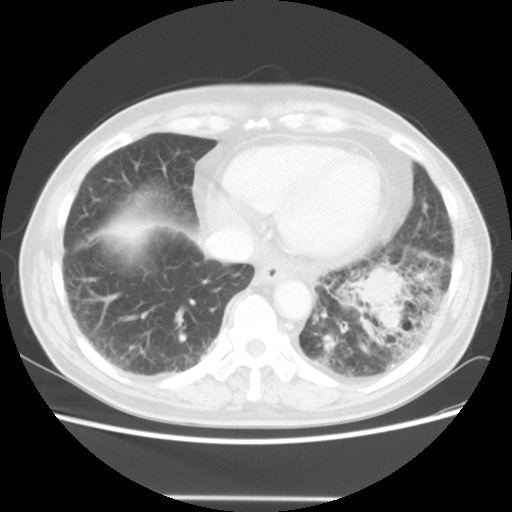
Chest CT, one axial slice. Slice 13 of 56 in the series (ordered by position). Lung window (W 1500 / L -600 HU). 512 × 512 image matrix, field of view 360 × 360 mm. Male patient, age 66 years. Case-level facts recorded for this patient, not image findings: clinical TNM (as recorded): T4 N3 M0; histopathological grade: G3.
Annotated regions visible in this slice (rectangle marked by the reading radiologist):
- lung tumour (recorded histology: small cell carcinoma): bounding box [x1, y1, x2, y2] px = [340, 262, 412, 346]